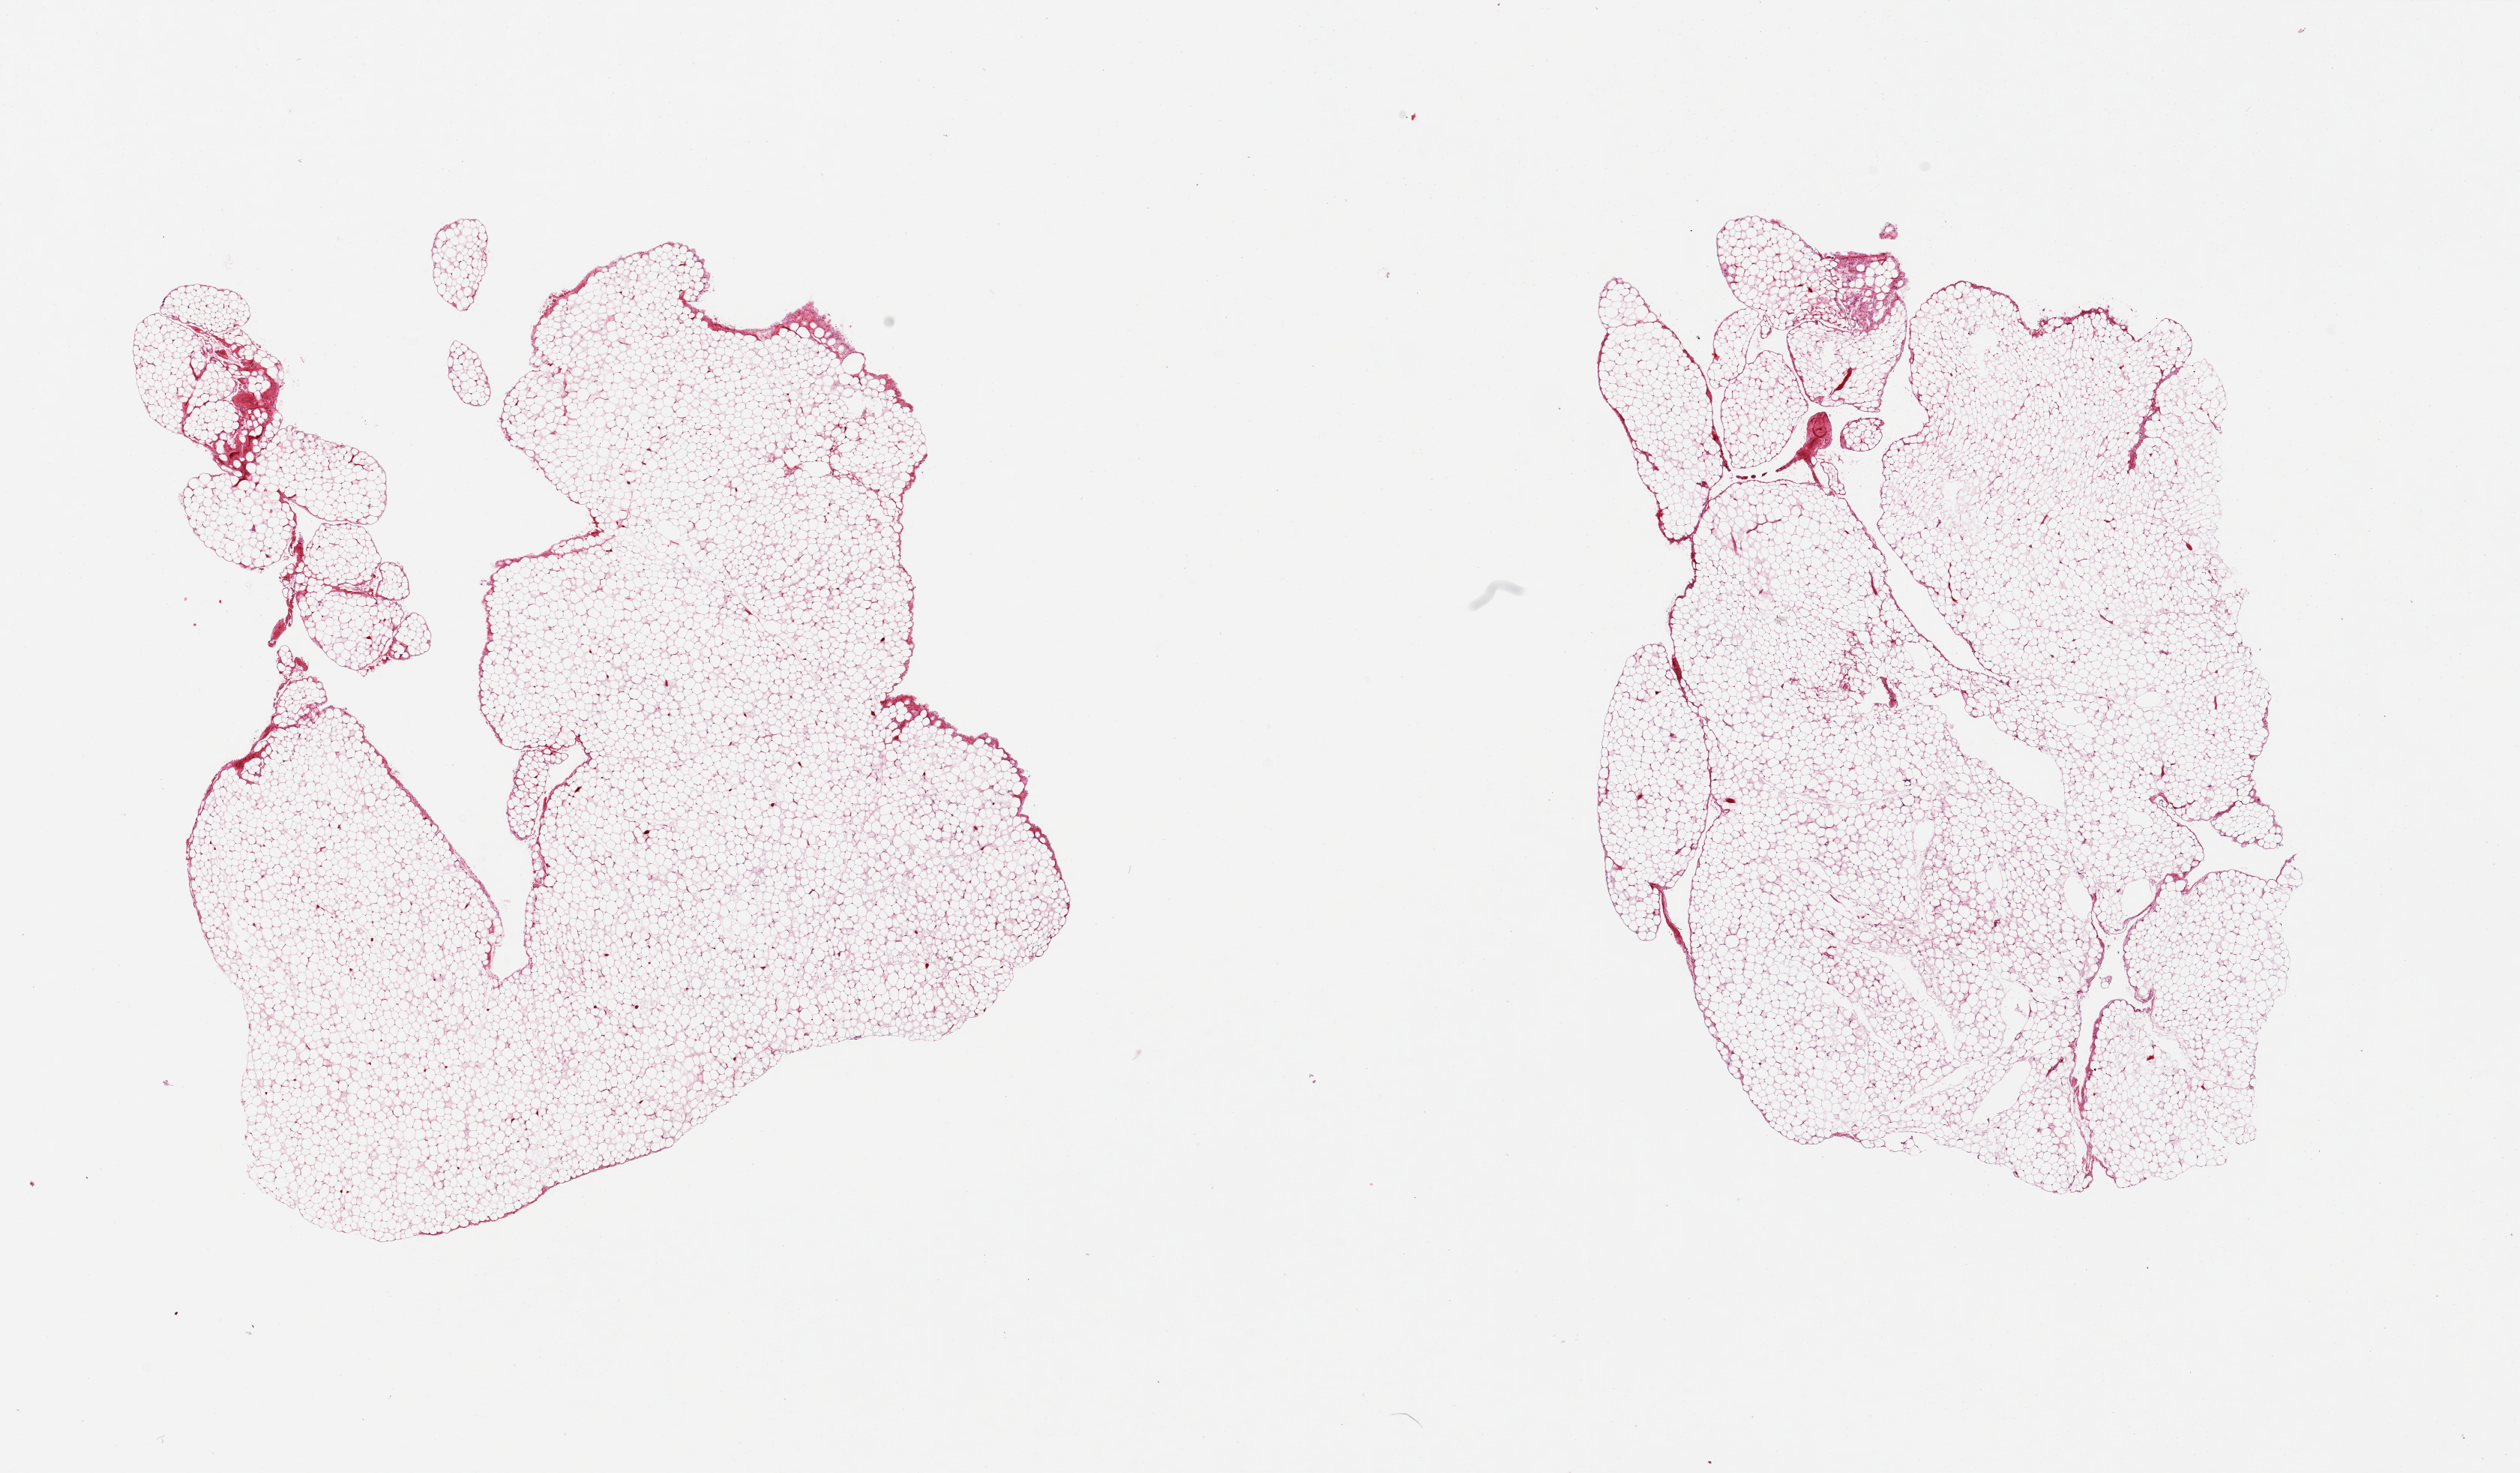
Whole-slide image, haematoxylin and eosin stain, low-resolution overview of the scanned area, about 26.6 x 15.5 mm (slide scanned at 20x). PAXgene-fixed, paraffin-embedded tissue. Sampled site (target tissue): omentum. Donor tissue sample.
Review note (as recorded): 2 pieces, virtually no vessels, good specimens.